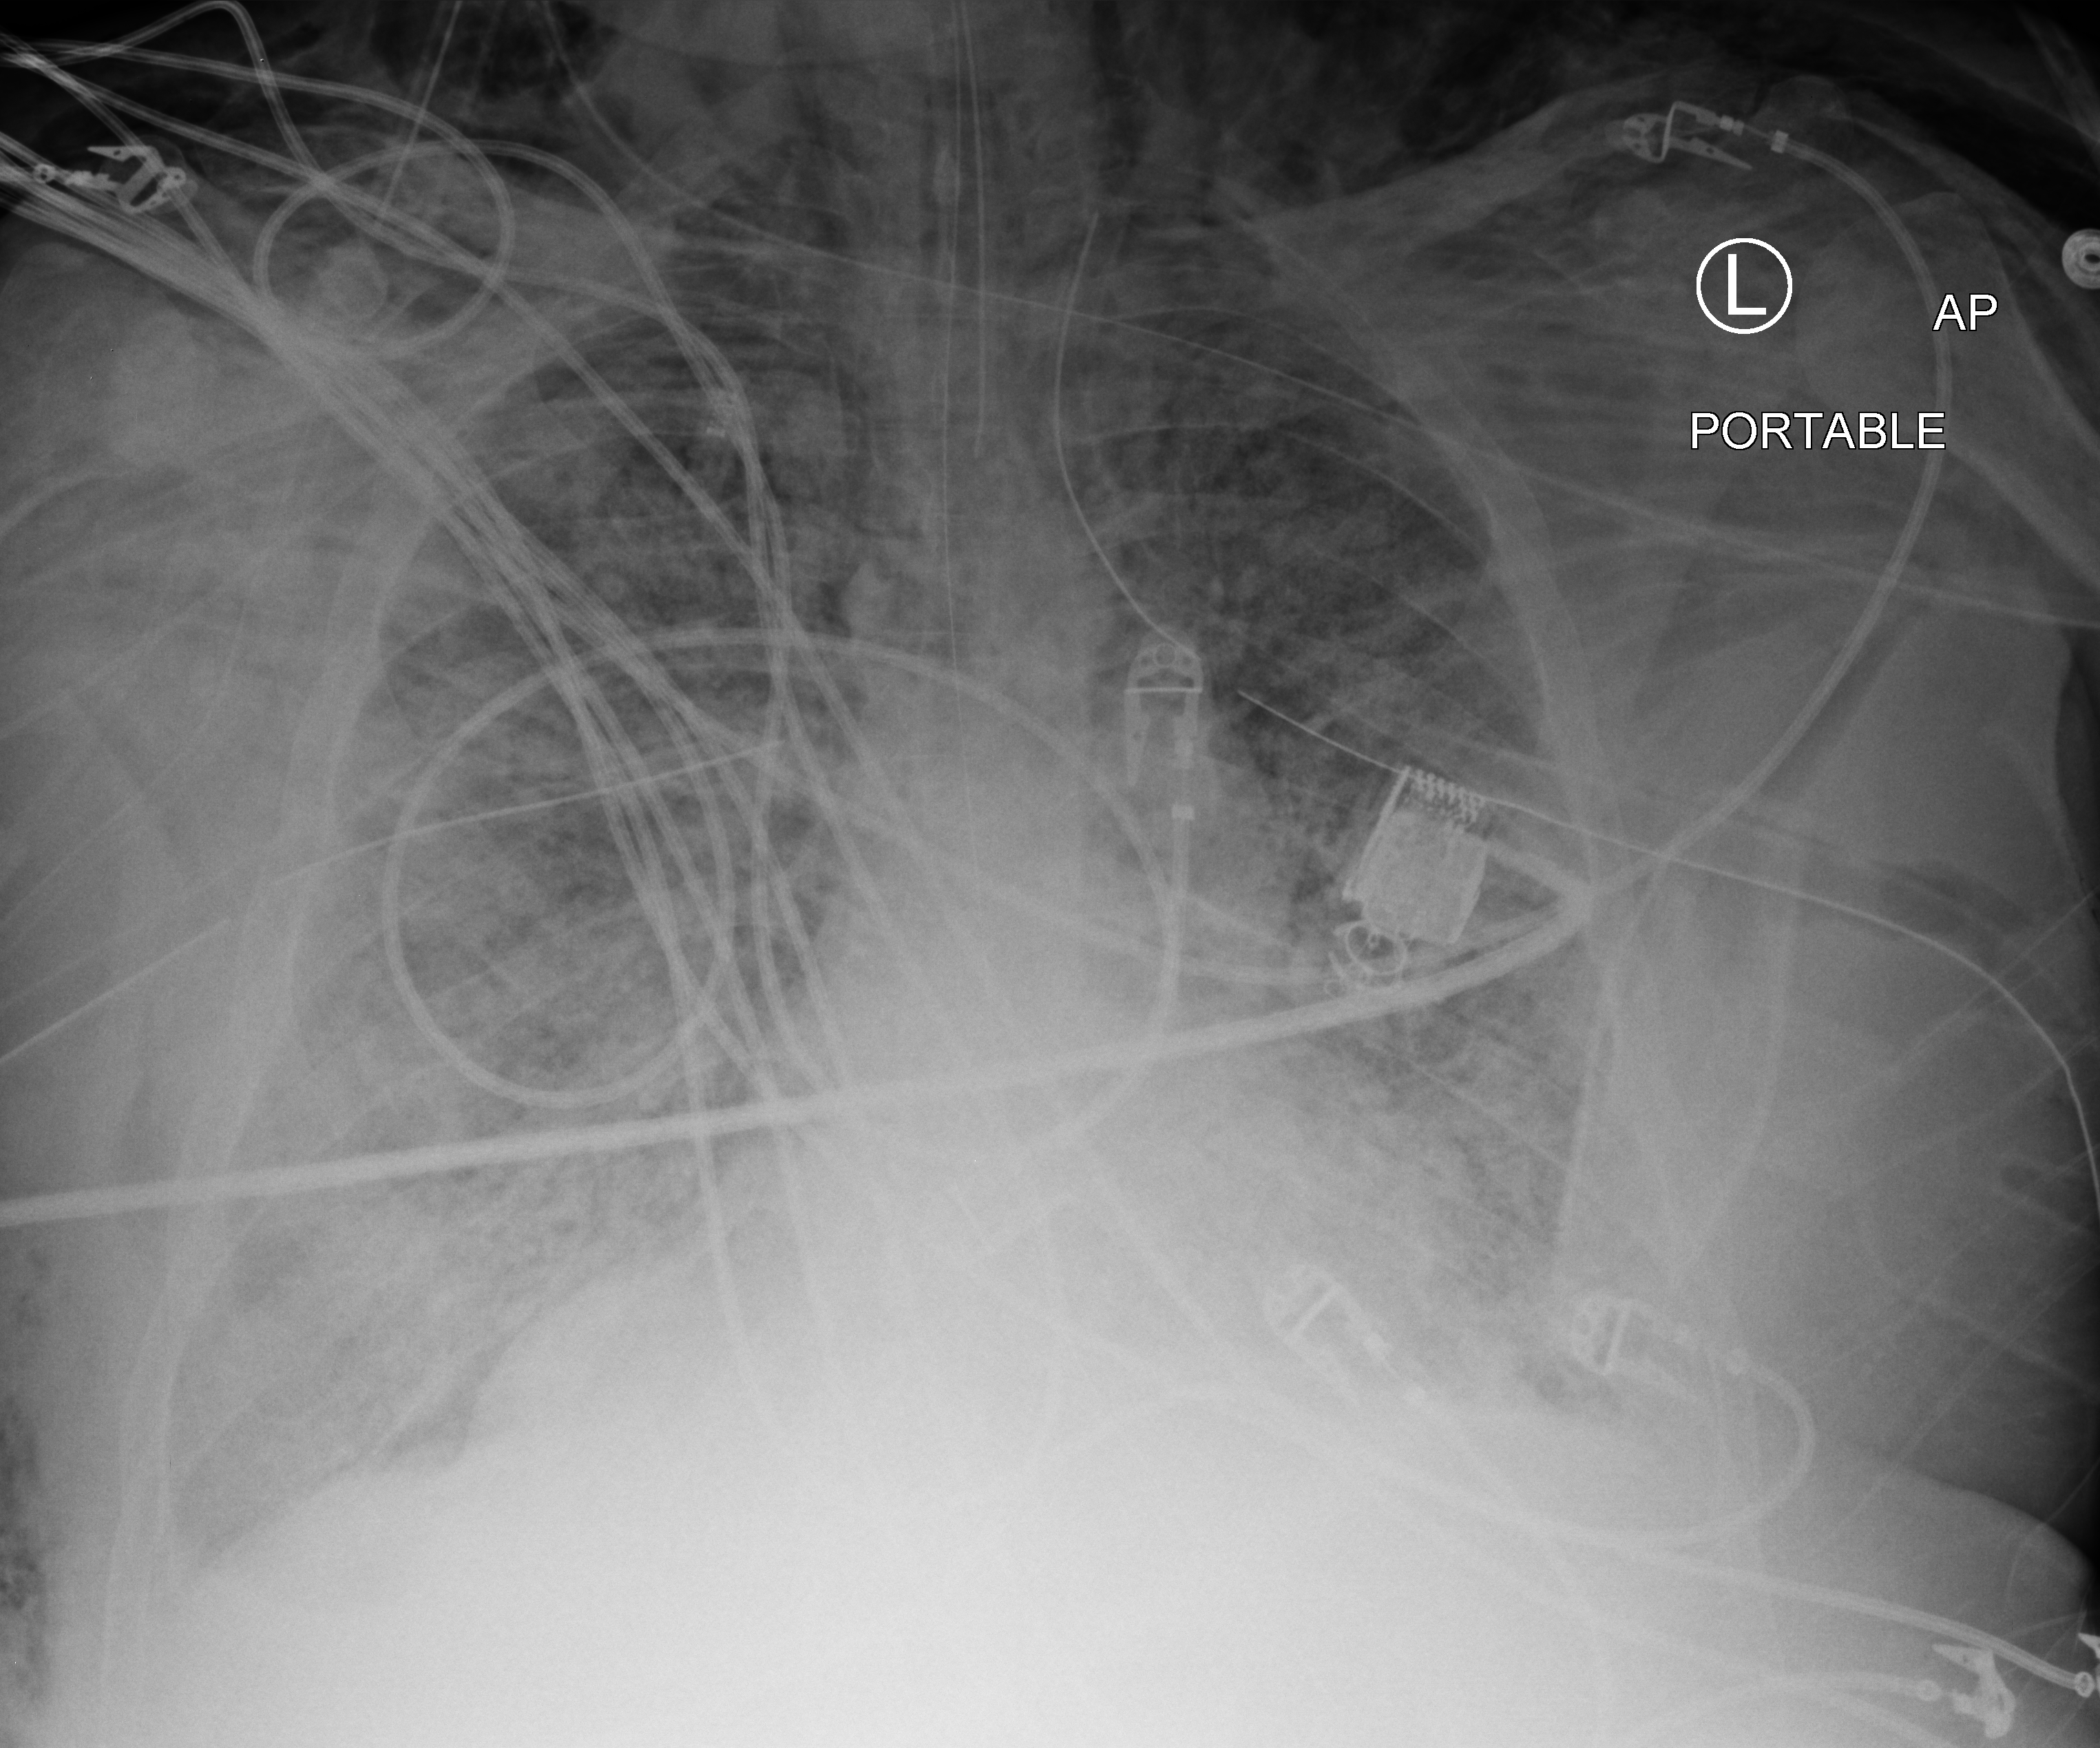
Chest X-ray (portable); anteroposterior (AP) projection. Adult patient hospitalised with COVID-19, age 18–59 years.
From the hospital-stay record, not from the radiograph (when in the stay this image was taken is not recorded):
- mechanically ventilated during this hospital stay: yes